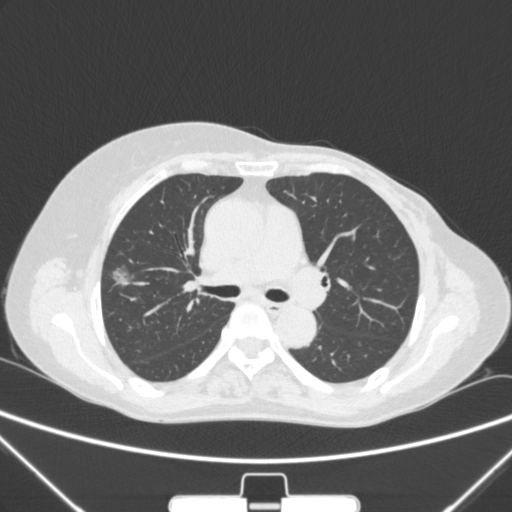
Chest CT, one axial slice. 120 kVp. Lung window (W 1500 / L -600 HU). 512 × 512 image matrix, field of view 350 × 350 mm. Female patient, age 64 years. Case-level facts recorded for this patient, not image findings: clinical TNM (as recorded): T1c N0 M0; histopathological grade: G1-2.
Structures marked on this image (rectangle marked by the reading radiologist):
- lung tumour (recorded histology: adenocarcinoma): bounding box [x1, y1, x2, y2] px = [105, 258, 142, 292]